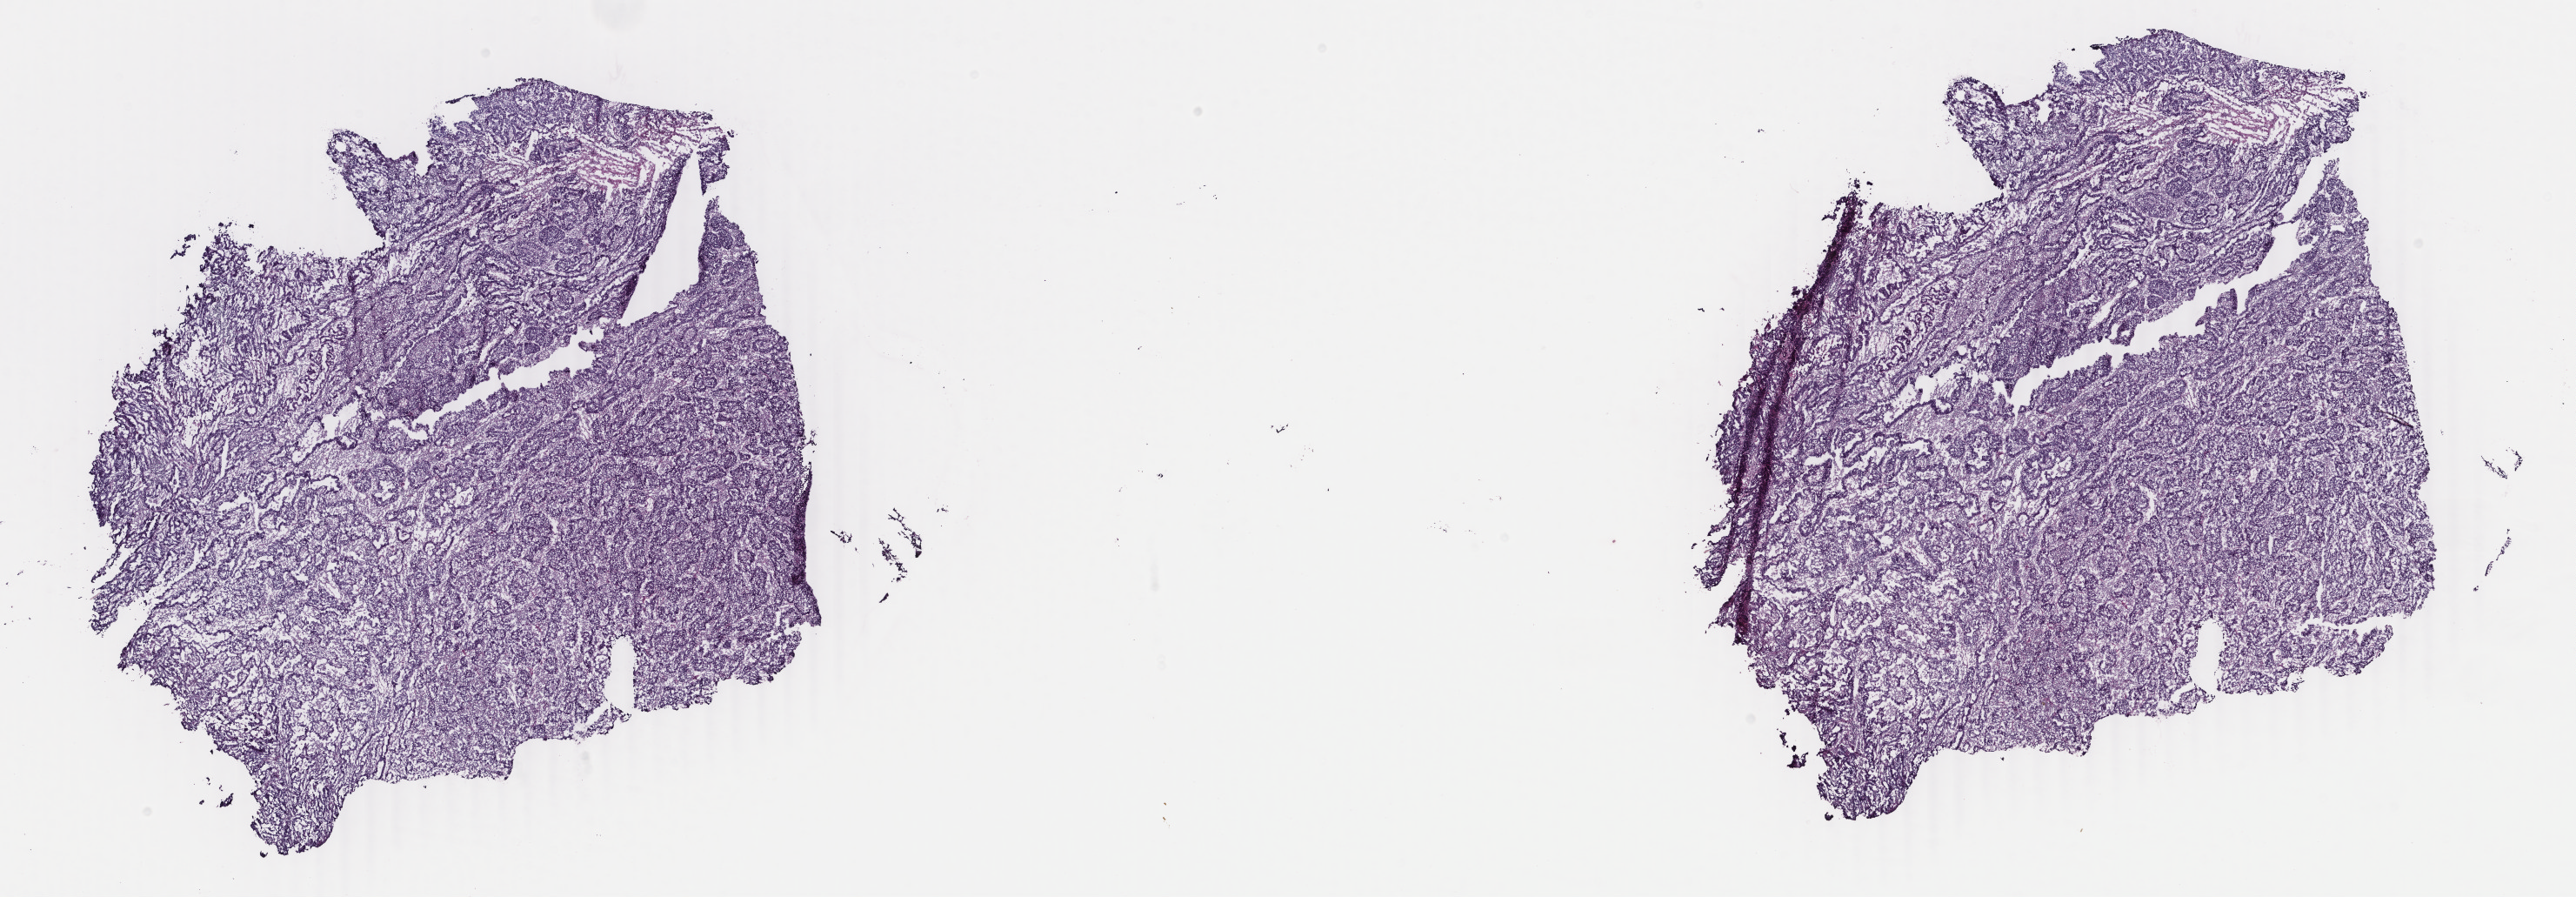
H&E whole-slide image — whole scanned area (about 23.6 x 8.2 mm, from a 40x scan) shown as a low-resolution overview. Frozen section. Sample: primary tumour, uterus. Patient: female, age at initial diagnosis 65 years. Histologic grade: G3 (poorly differentiated). Composition of this section per pathologist review: tumour cells 92%, tumour nuclei 92%, normal cells 0%, stromal cells 3%, necrosis 5%. Inflammatory infiltration, as recorded: lymphocyte infiltration 30%, monocyte infiltration 30%, neutrophil infiltration 3%.
FIGO stage: IVB. Pathologic diagnosis: Adenocarcinoma, NOS (endometrium). Lymph nodes positive (case pathology): 0 of 7 examined.